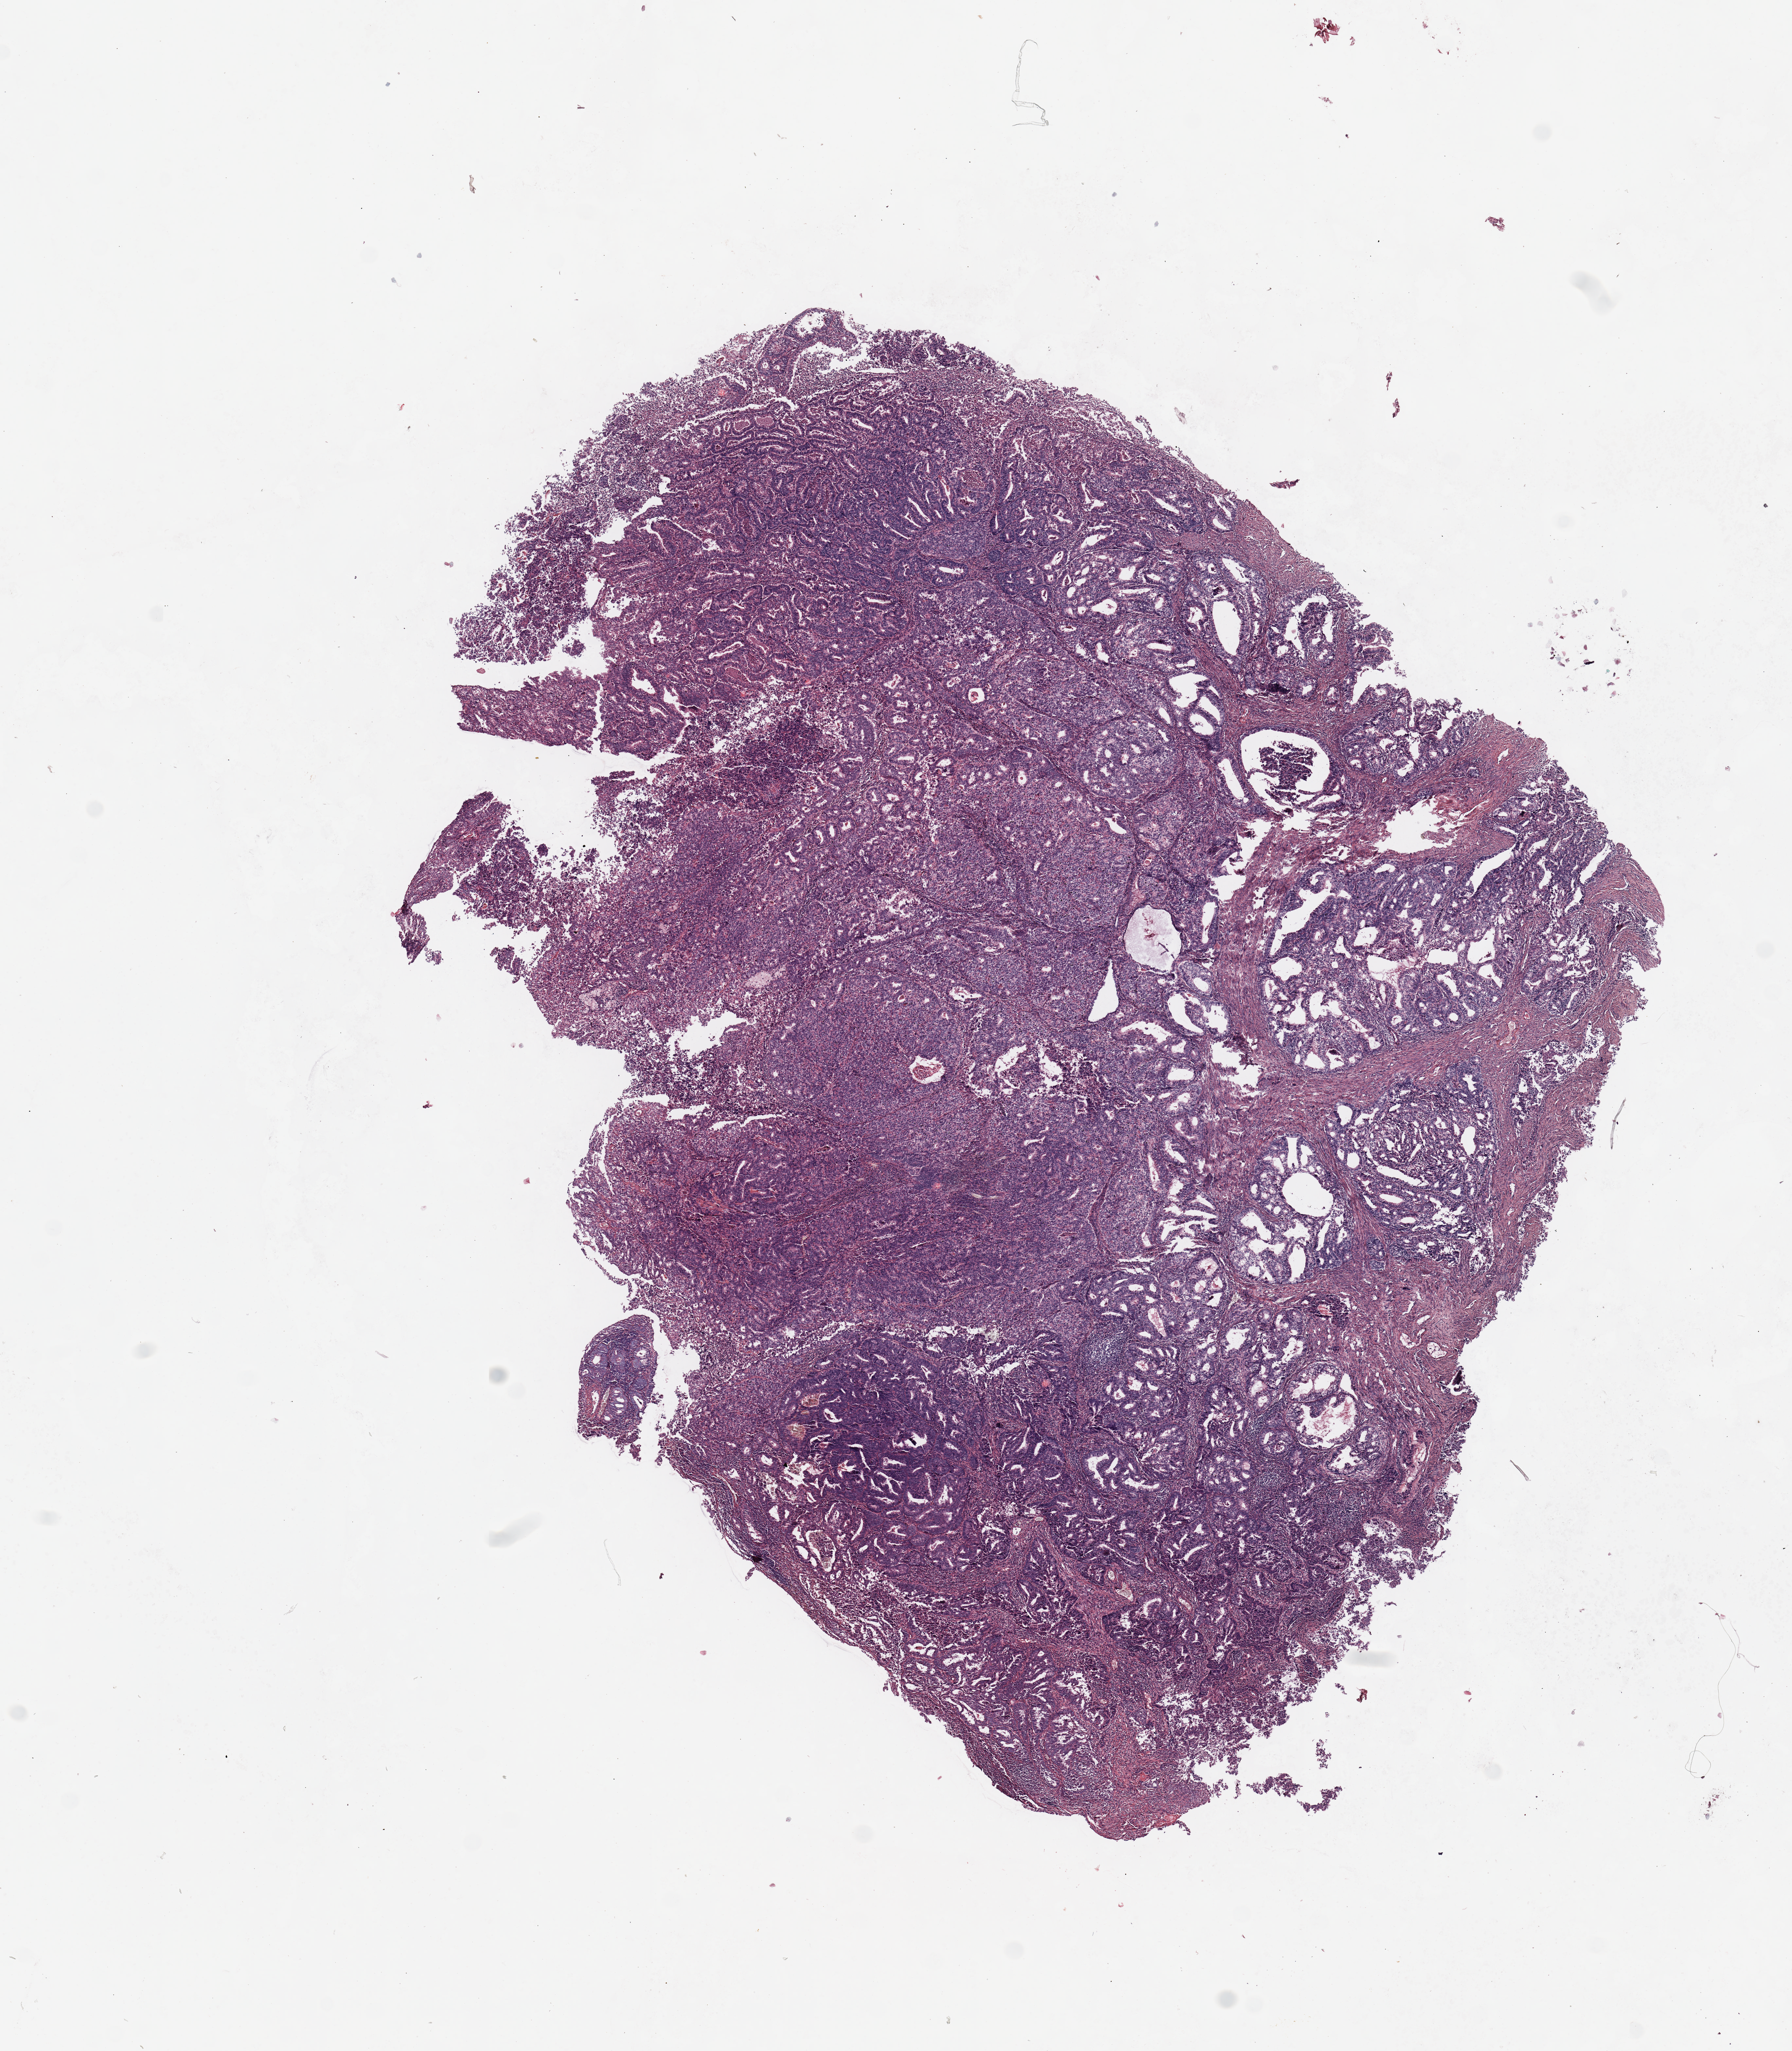
Hematoxylin and eosin (H&E) stained whole-slide image — whole scanned area (about 10.8 x 12.4 mm, acquisition: 20x scan) shown as a low-resolution overview; tumour tissue sample, uterus. Patient: female, age 70 years. Histologic grade: G2 (moderately differentiated).
* histologic diagnosis: Endometrioid adenocarcinoma, NOS
* AJCC pathologic stage: I